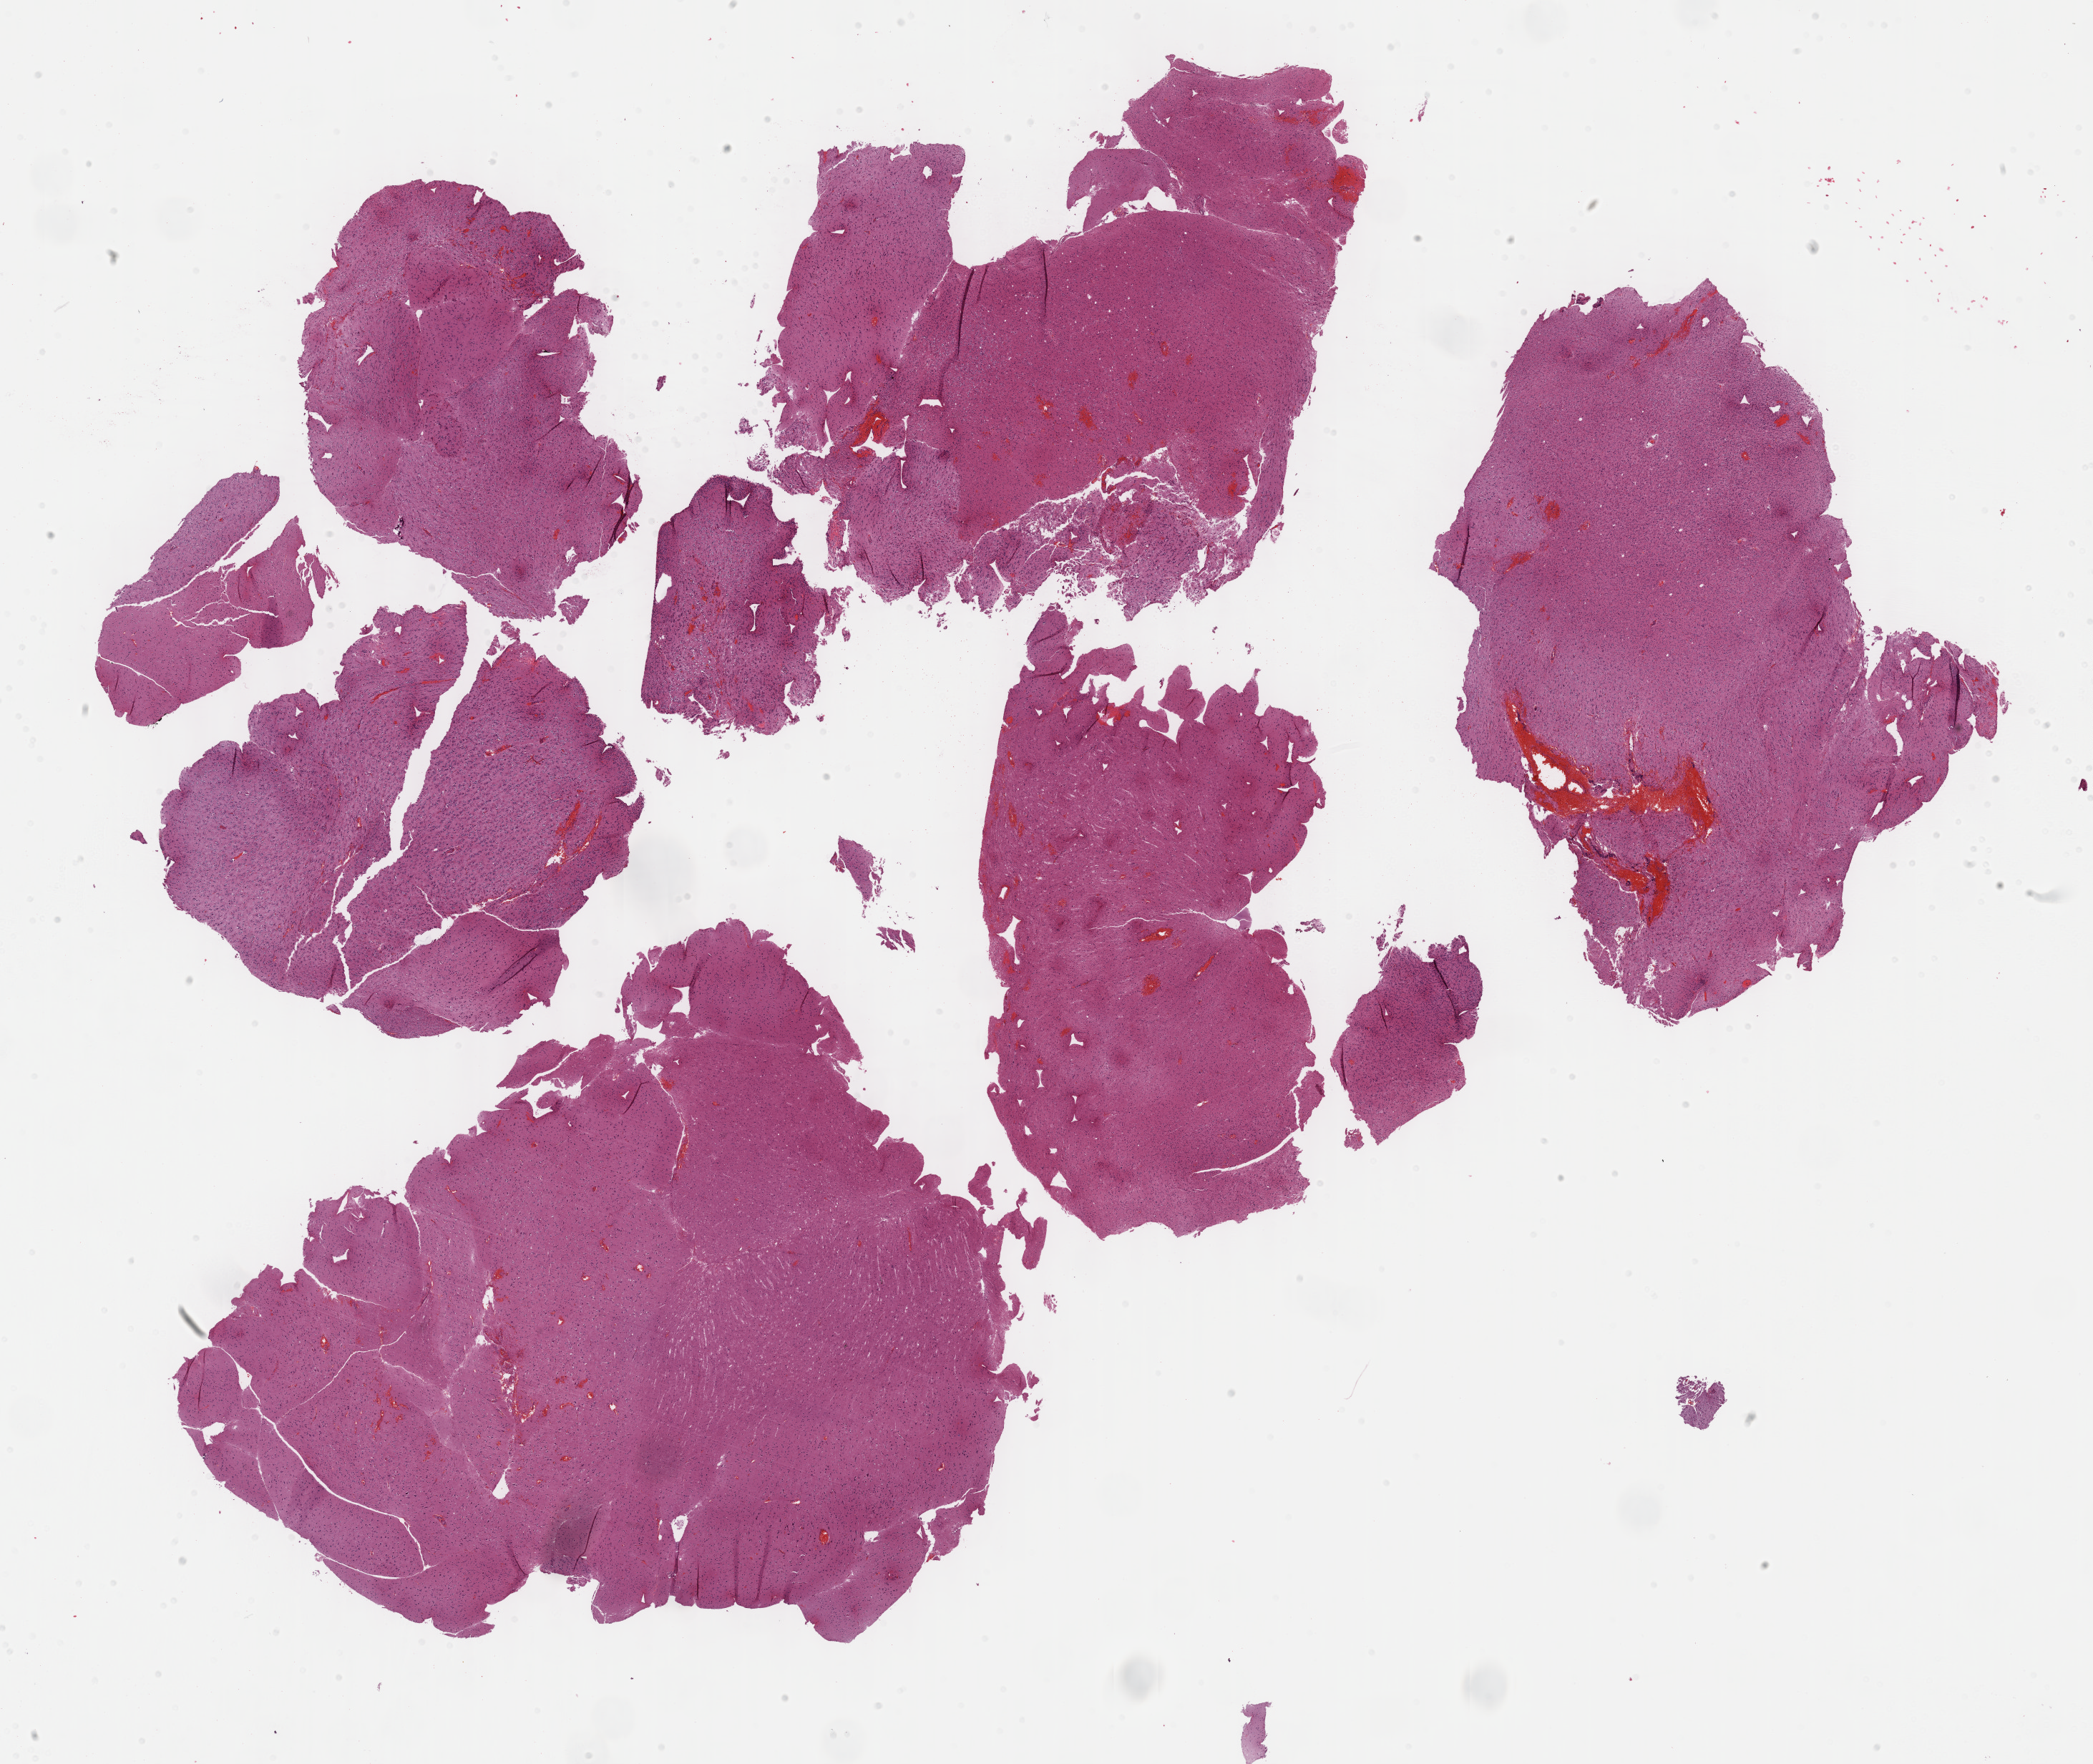
Digitized Hematoxylin and eosin (H&E) stained tissue section (whole slide), shown as a low-resolution overview of the whole scanned area (about 23.7 x 19.9 mm, acquisition: 40x scan). FFPE section. Primary tumour sample from the brain. Male patient; age at initial diagnosis 54 years. Histologic grade: G2 (moderately differentiated).
• histologic diagnosis: Oligodendroglioma, NOS
• laterality: right